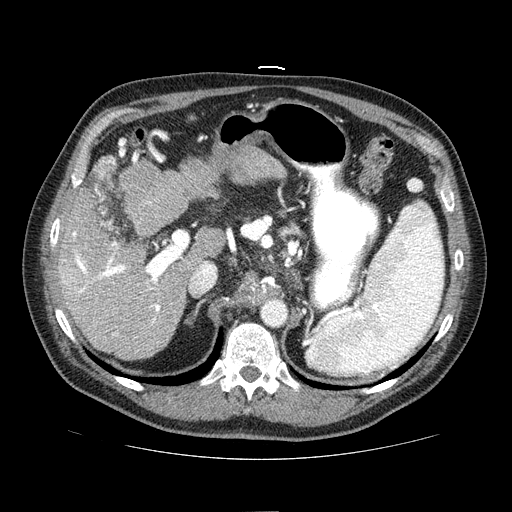
Contrast-enhanced abdominal CT (liver protocol), one axial slice. Slice 44 of 81 in the series (ordered by position). Reconstruction kernel STANDARD. 100 kVp. One of 2 acquisitions stored at this slice position. Soft-tissue window (W 400 / L 40 HU). 2.5 mm slice thickness. 512 × 512 image matrix, field of view 400 × 400 mm. From the clinical record (not read from this slice): diagnosis: hepatocellular carcinoma (patient treated with transarterial chemoembolisation; whether this scan precedes or follows treatment is not stated here); TNM stage (as recorded): Stage-IIIA; Child-Pugh class: A; tumour differentiation: well differentiated; tumour nodularity: multinodular.
Structures marked on this image (semi-automatically segmented with operator editing):
- liver parenchyma outside the tumour (the mass and vessels are separate outlines, so this box may not span the whole liver): bounding box (x1, y1, x2, y2) in pixels: (56, 183, 213, 360)
- liver vessels: (61, 188, 161, 336)